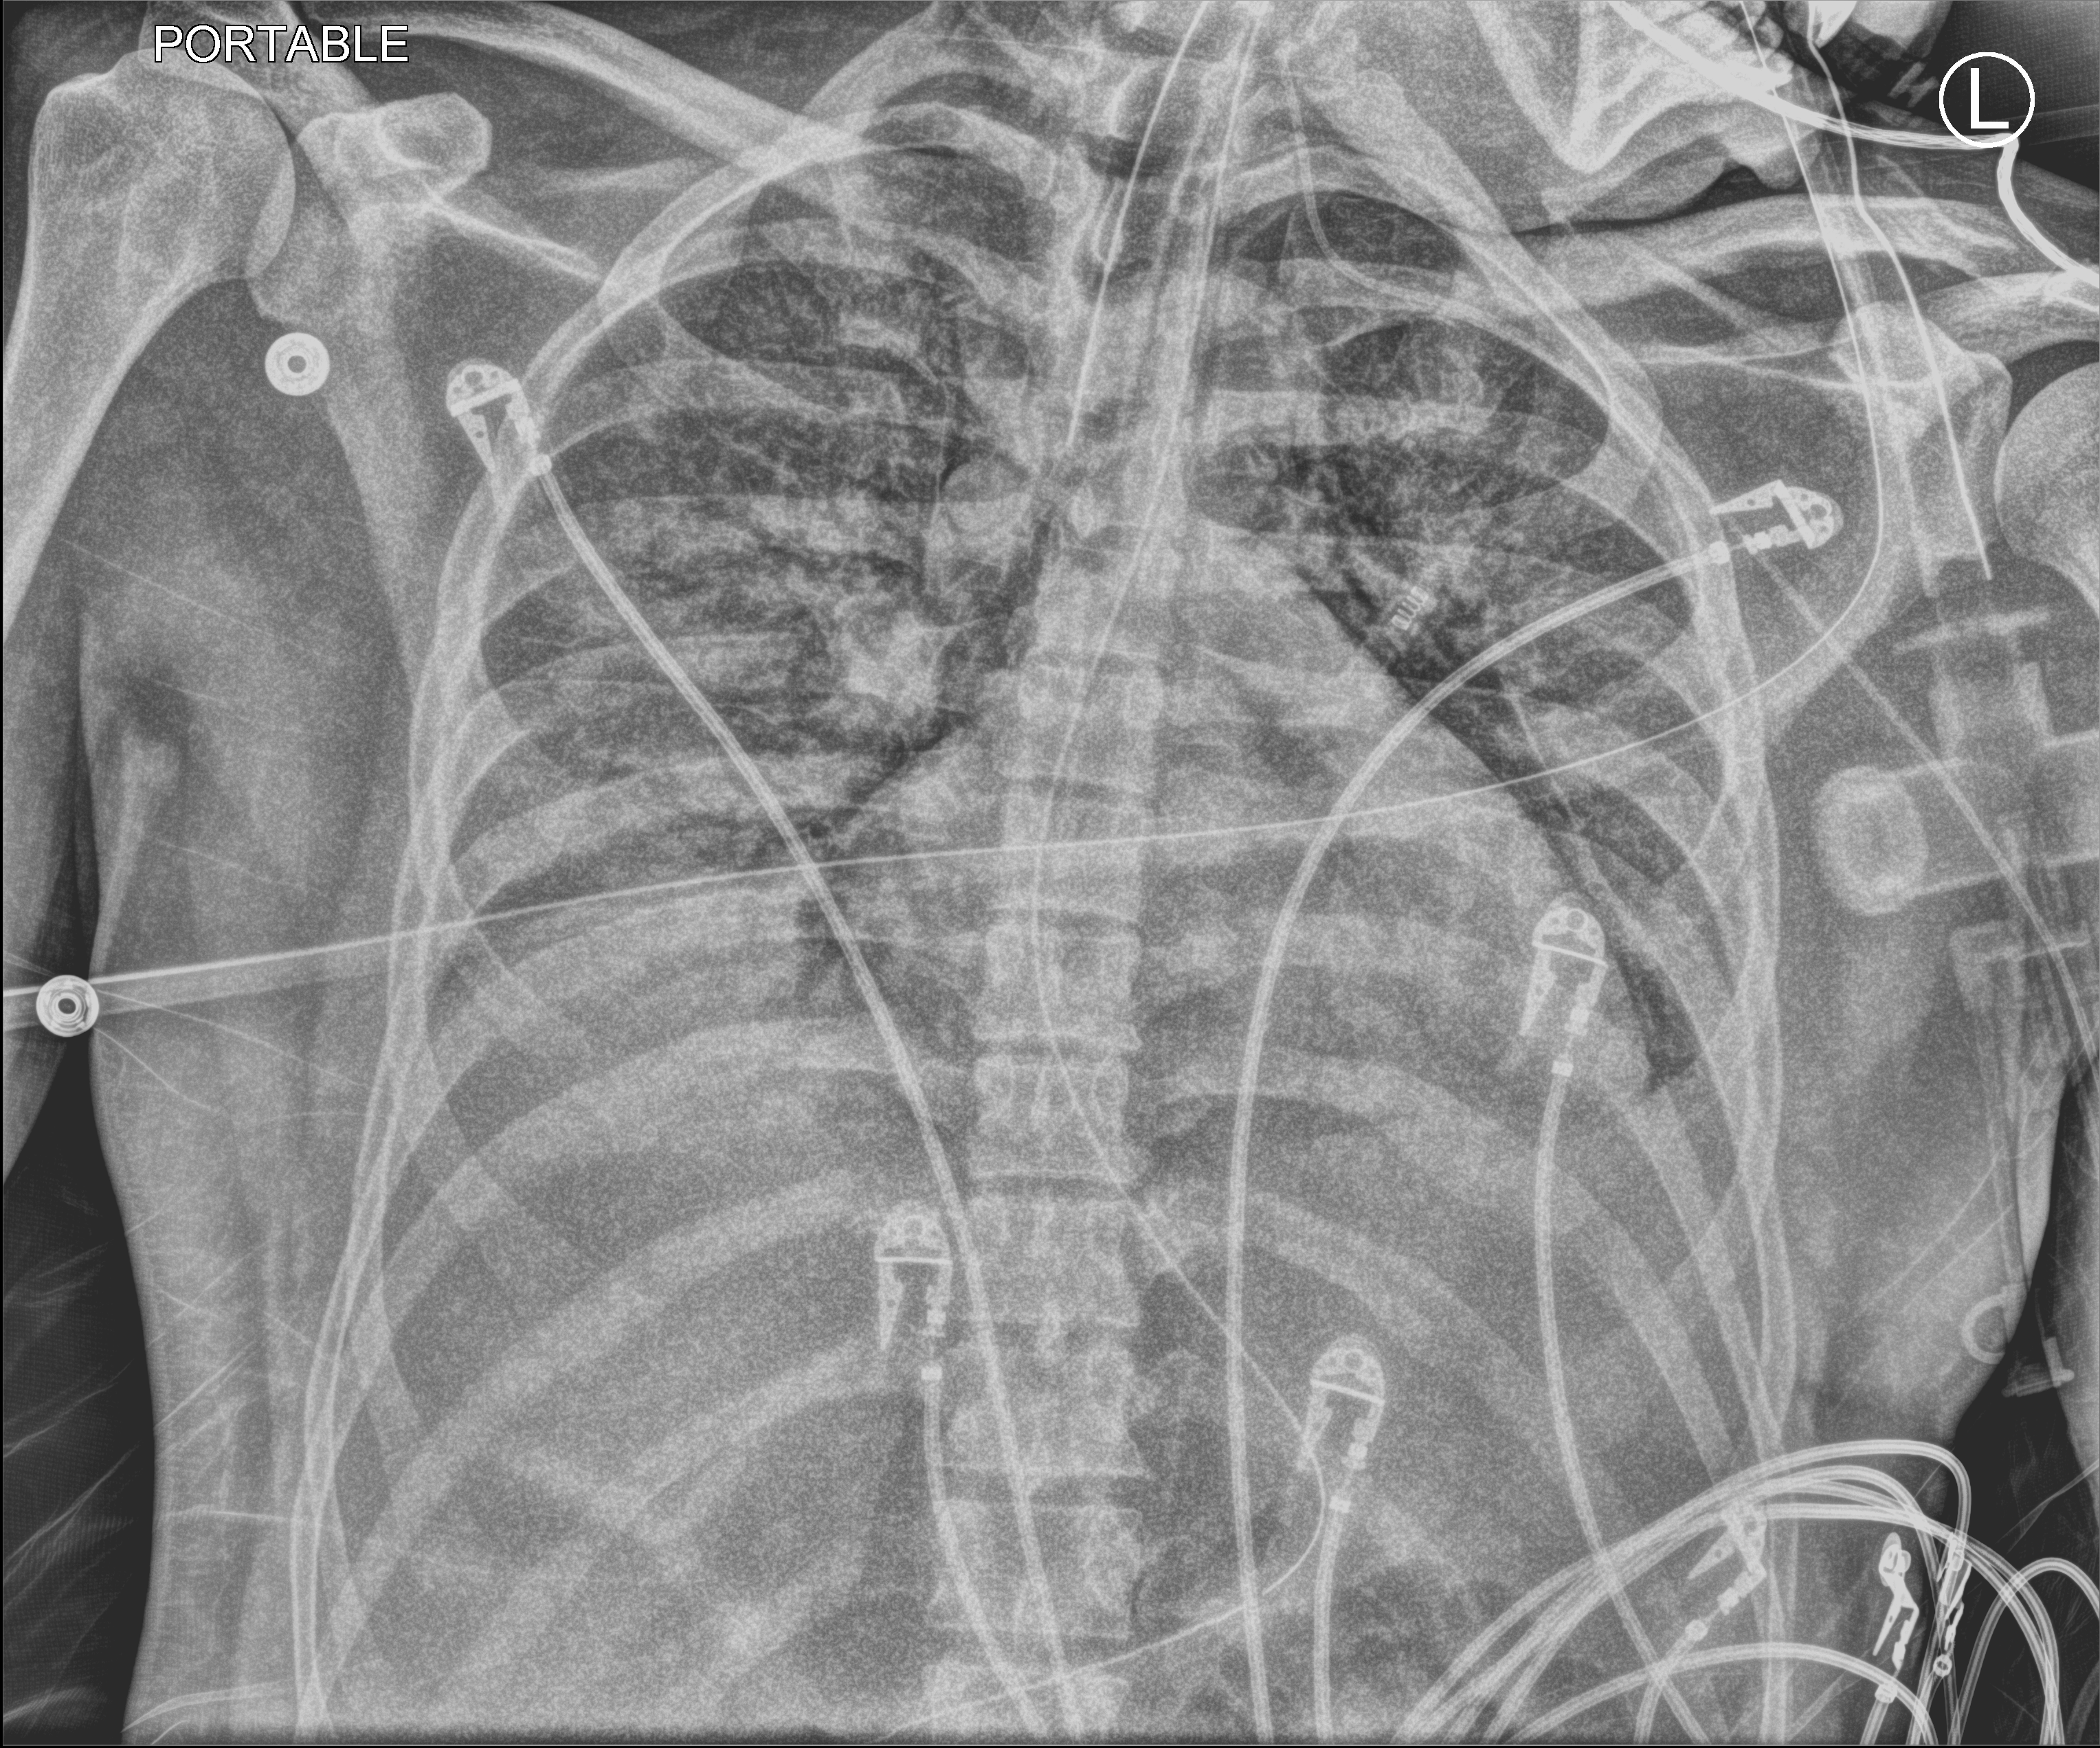
Bedside chest radiograph (computed radiography). Male patient hospitalised with COVID-19, age 18–59 years.
From the hospital-stay record, not from the radiograph (when in the stay this image was taken is not recorded): length of hospital stay: 30 days; mechanically ventilated during this hospital stay: yes; COPD (admission record): no.